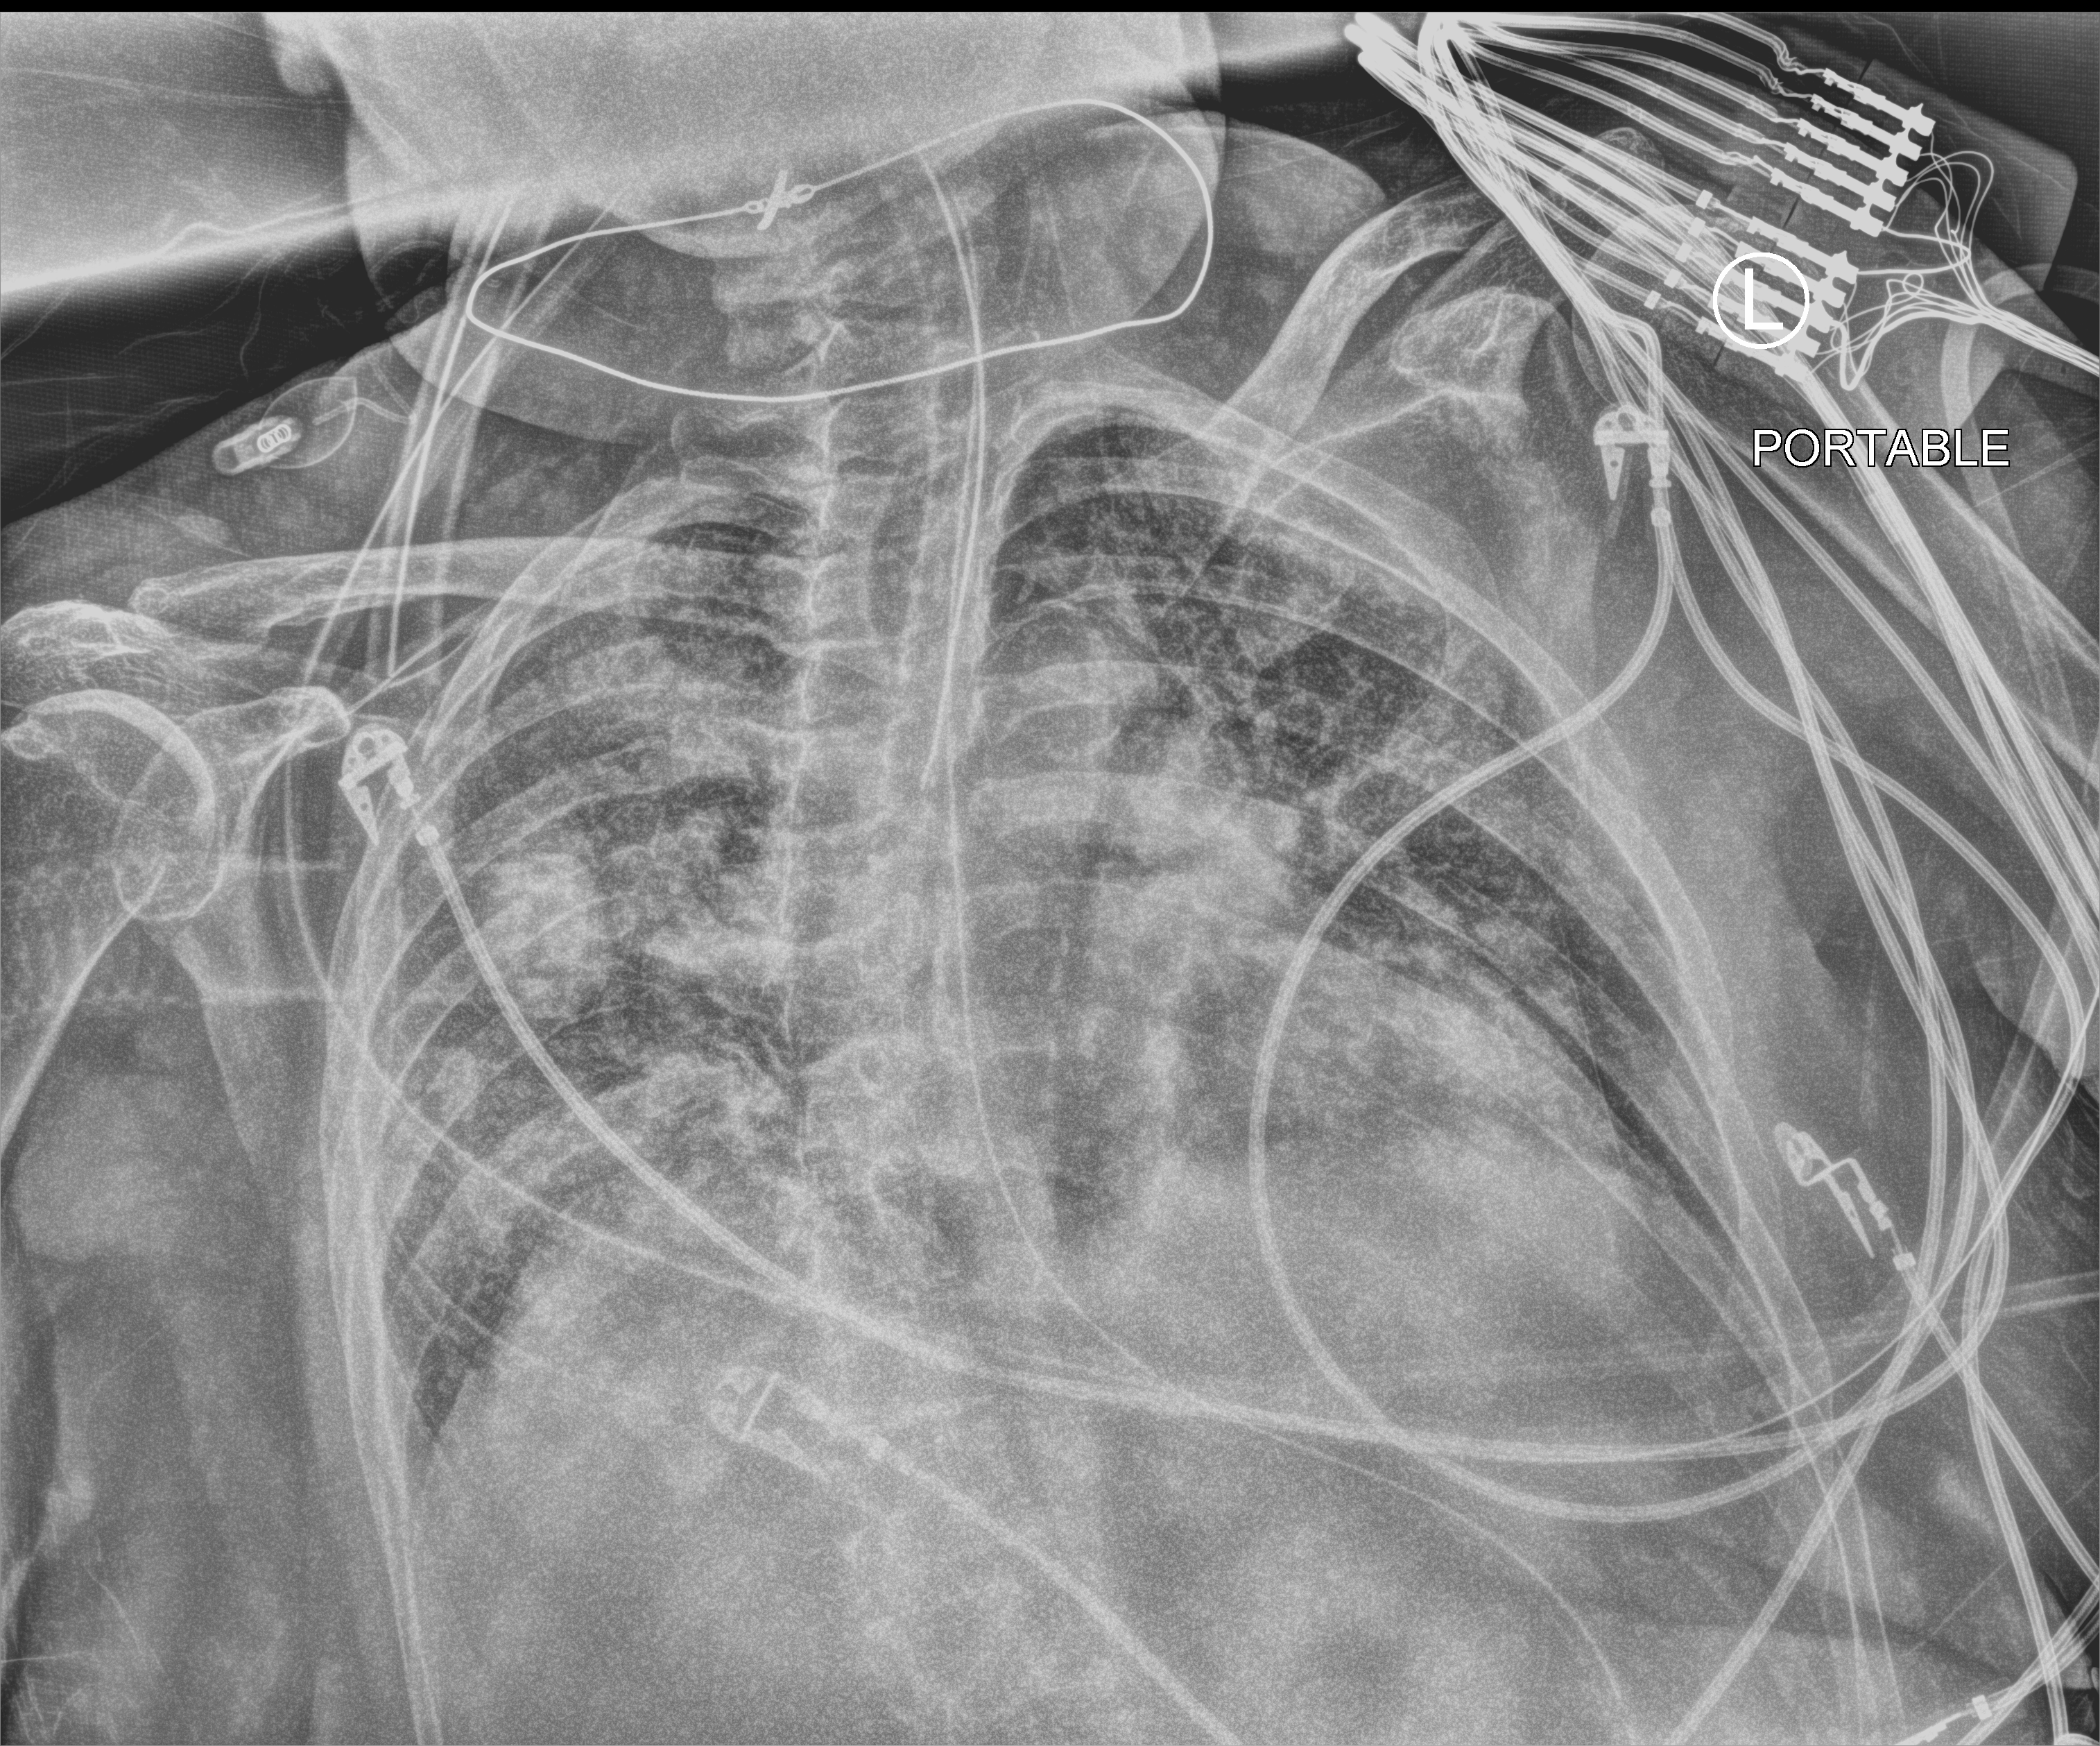
Chest X-ray (portable); anteroposterior (AP) projection. Patient hospitalised with COVID-19; female, aged 75–90 years.
Hospital-stay facts (about this admission, not read from this image; timing relative to this image not recorded): mechanically ventilated during this hospital stay: yes; chronic kidney disease (admission record): no.